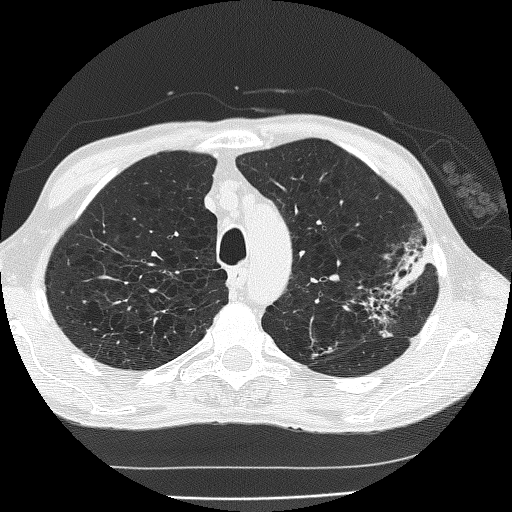
Axial slice from a low-dose chest CT screening exam. Second screening round (one year after baseline). Lung window (W 1500 / L -600 HU). Lung (sharp) reconstruction kernel (FC51). Slice 43 of 185 in the series. Male, age 60 years at enrolment. Current smoker at enrolment.
- Expert reader's lesion annotation, bounding box <346,246,438,337> (left, top, right, bottom; pixels).
- The screening reader recorded 2 non-calcified nodules or masses ≥4 mm on this exam; which of them this box marks is not recorded.
- Official screen result: positive, other.
- Lung cancer was diagnosed 178 days after this screen: bronchiolo-alveolar carcinoma, mucinous, left upper lobe, stage IV (AJCC 6th edition).